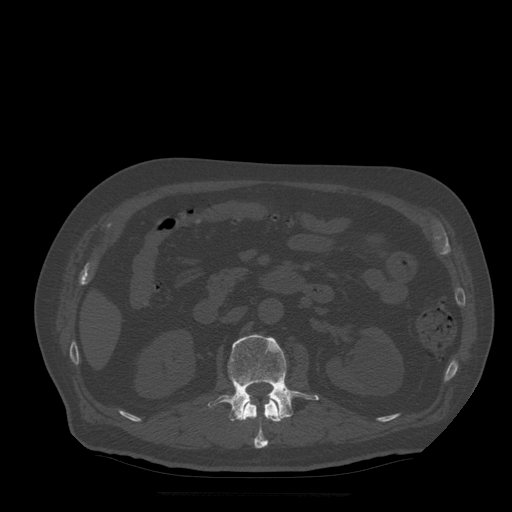
CT including the spine, one axial slice. Slice 177 of 522 in the series (ordered by position). Bone window (W 1800 / L 400 HU). 1.25 mm slice thickness. 512 × 512 image matrix, field of view 420 × 420 mm. Patient age 72 years. From the clinical record (not read from this slice): primary cancer: prostate.
Annotated regions visible in this slice (semi-automatically segmented with operator editing):
- L1 vertebra: box from (x=242, y=397) to (x=281, y=449) px
- L2 vertebra: (x=208, y=335)–(x=319, y=421)